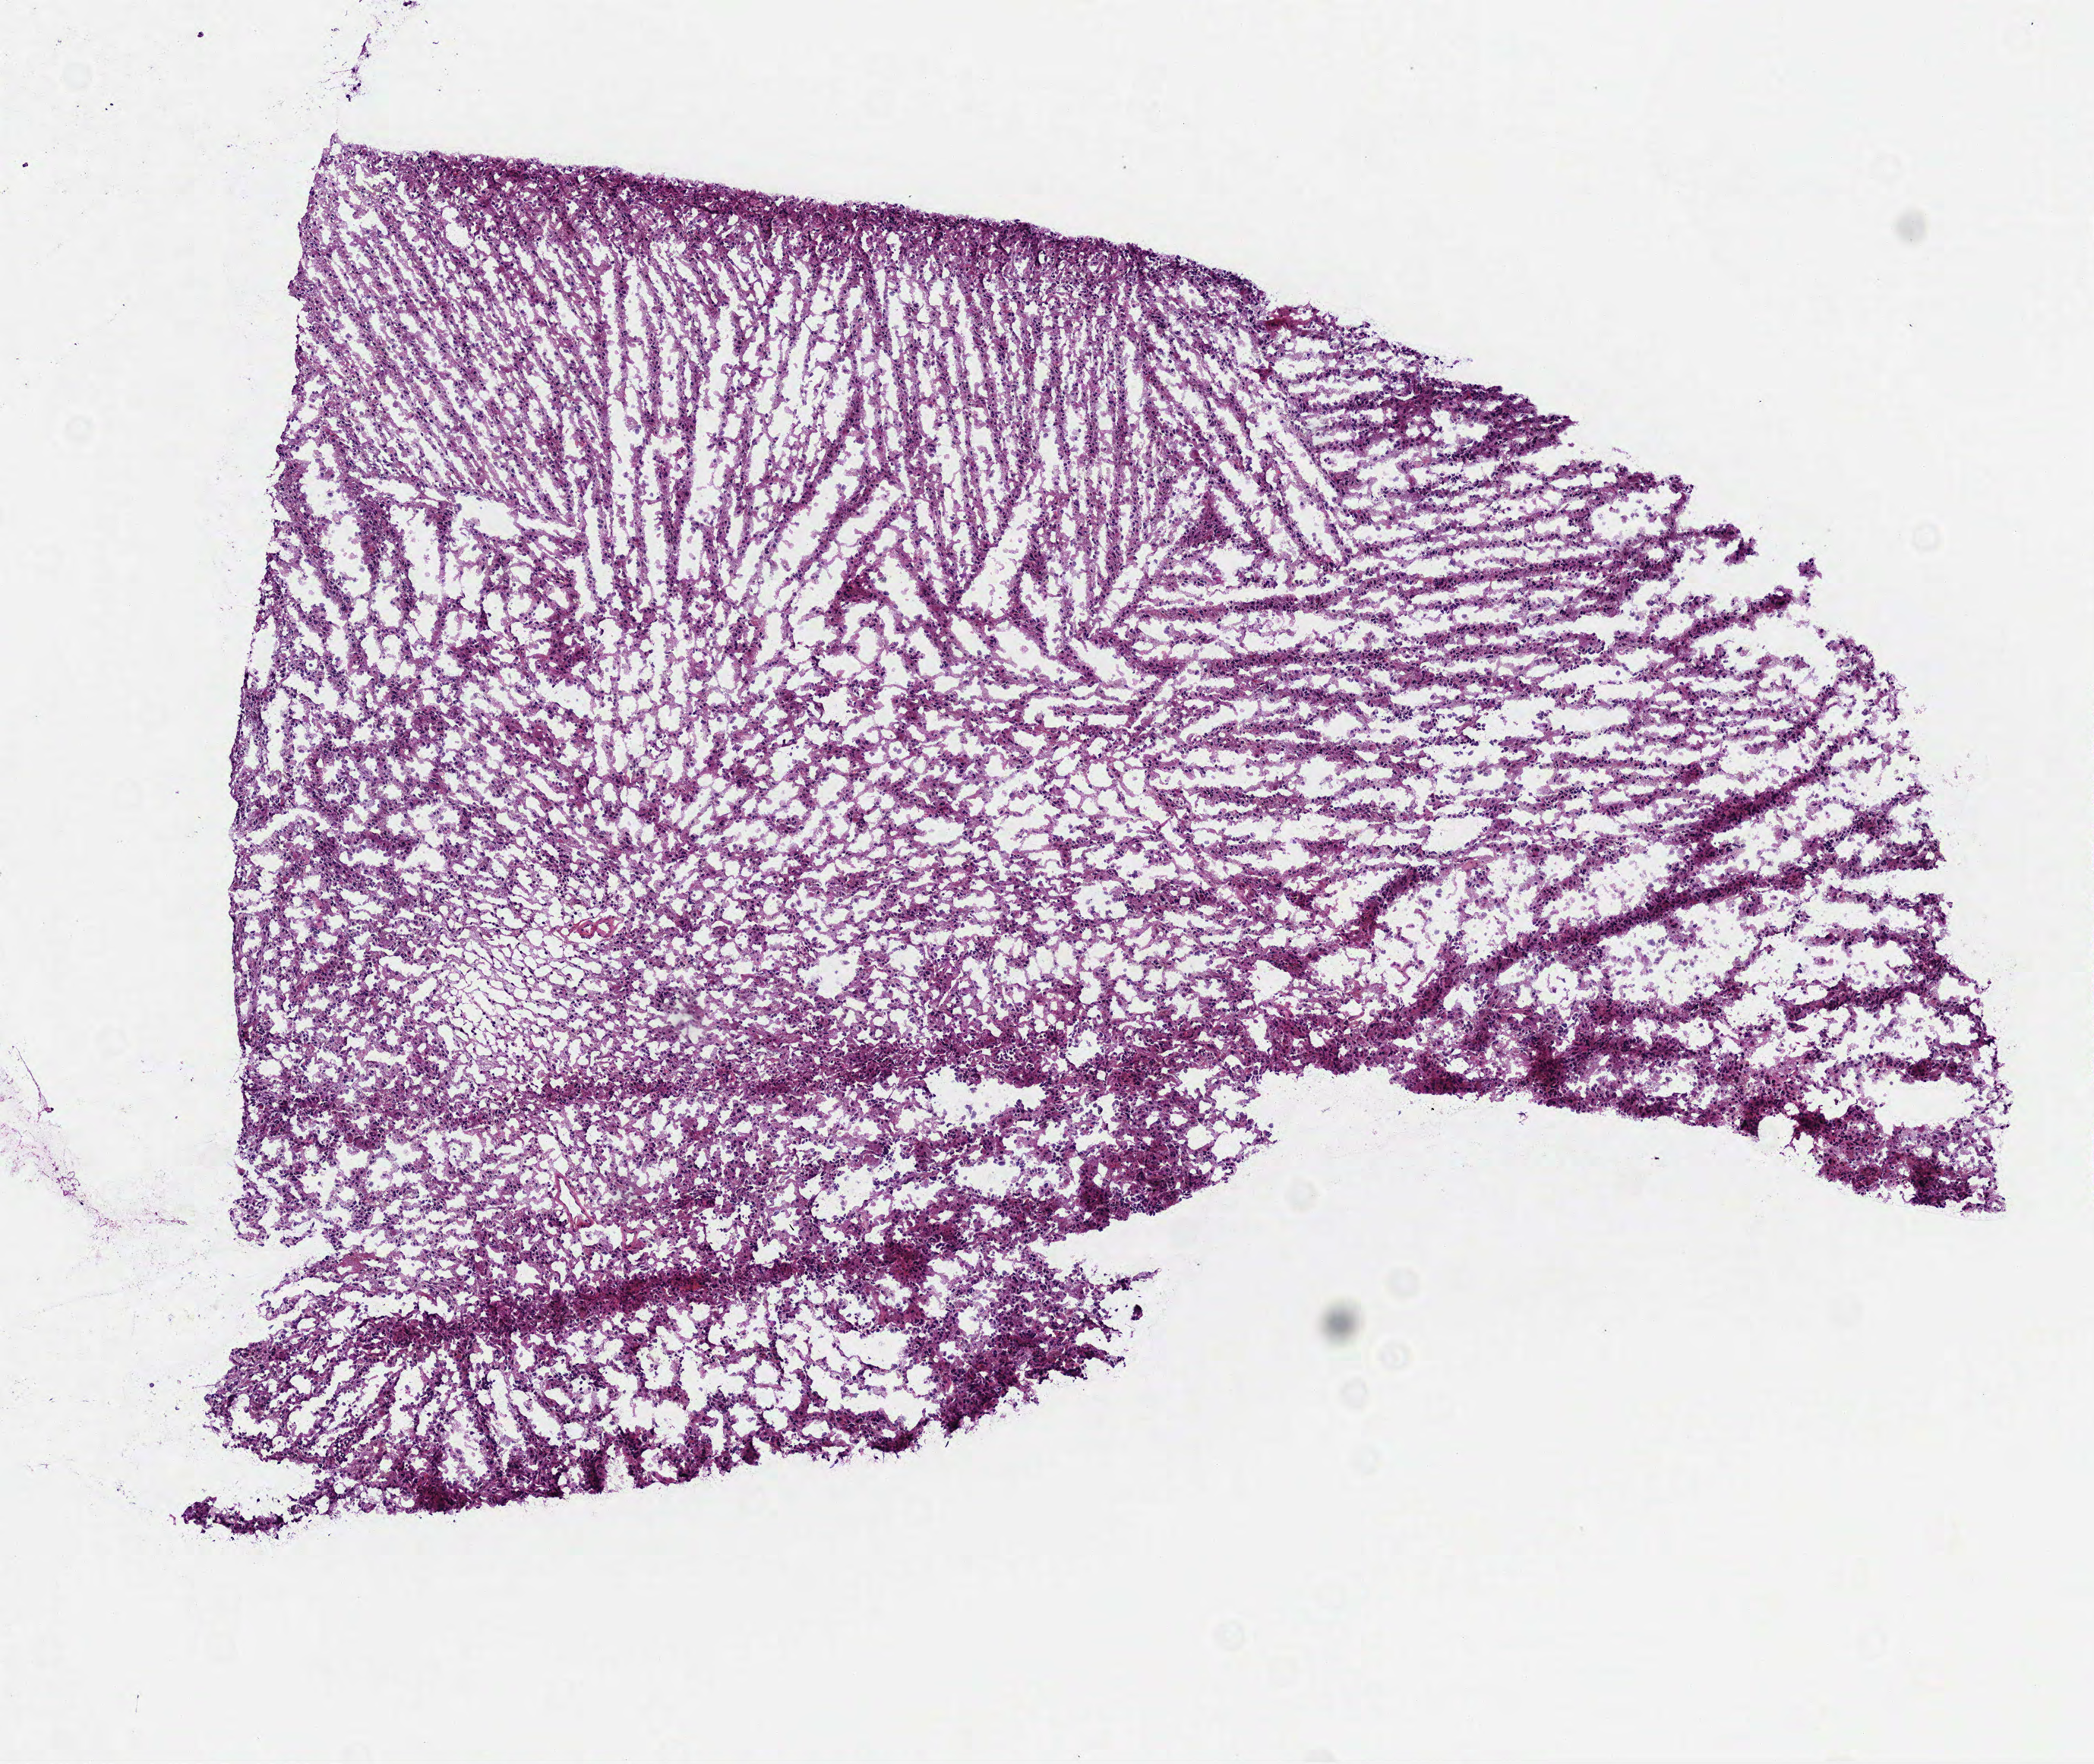
Digitized Hematoxylin and eosin (H&E) stained tissue section (whole slide), whole scanned area (about 5.6 x 4.7 mm) shown as a low-resolution overview, frozen section from the top of the tissue portion, brain, primary tumour sample. Male, age 43 years at initial diagnosis. Histologic grade: G2 (moderately differentiated). Pathologist review of this section (percent, as recorded): tumour cells 100%, tumour nuclei 80%, normal cells 0%, stromal cells 0%, necrosis 0%.
Histologic diagnosis: Oligodendroglioma, NOS.